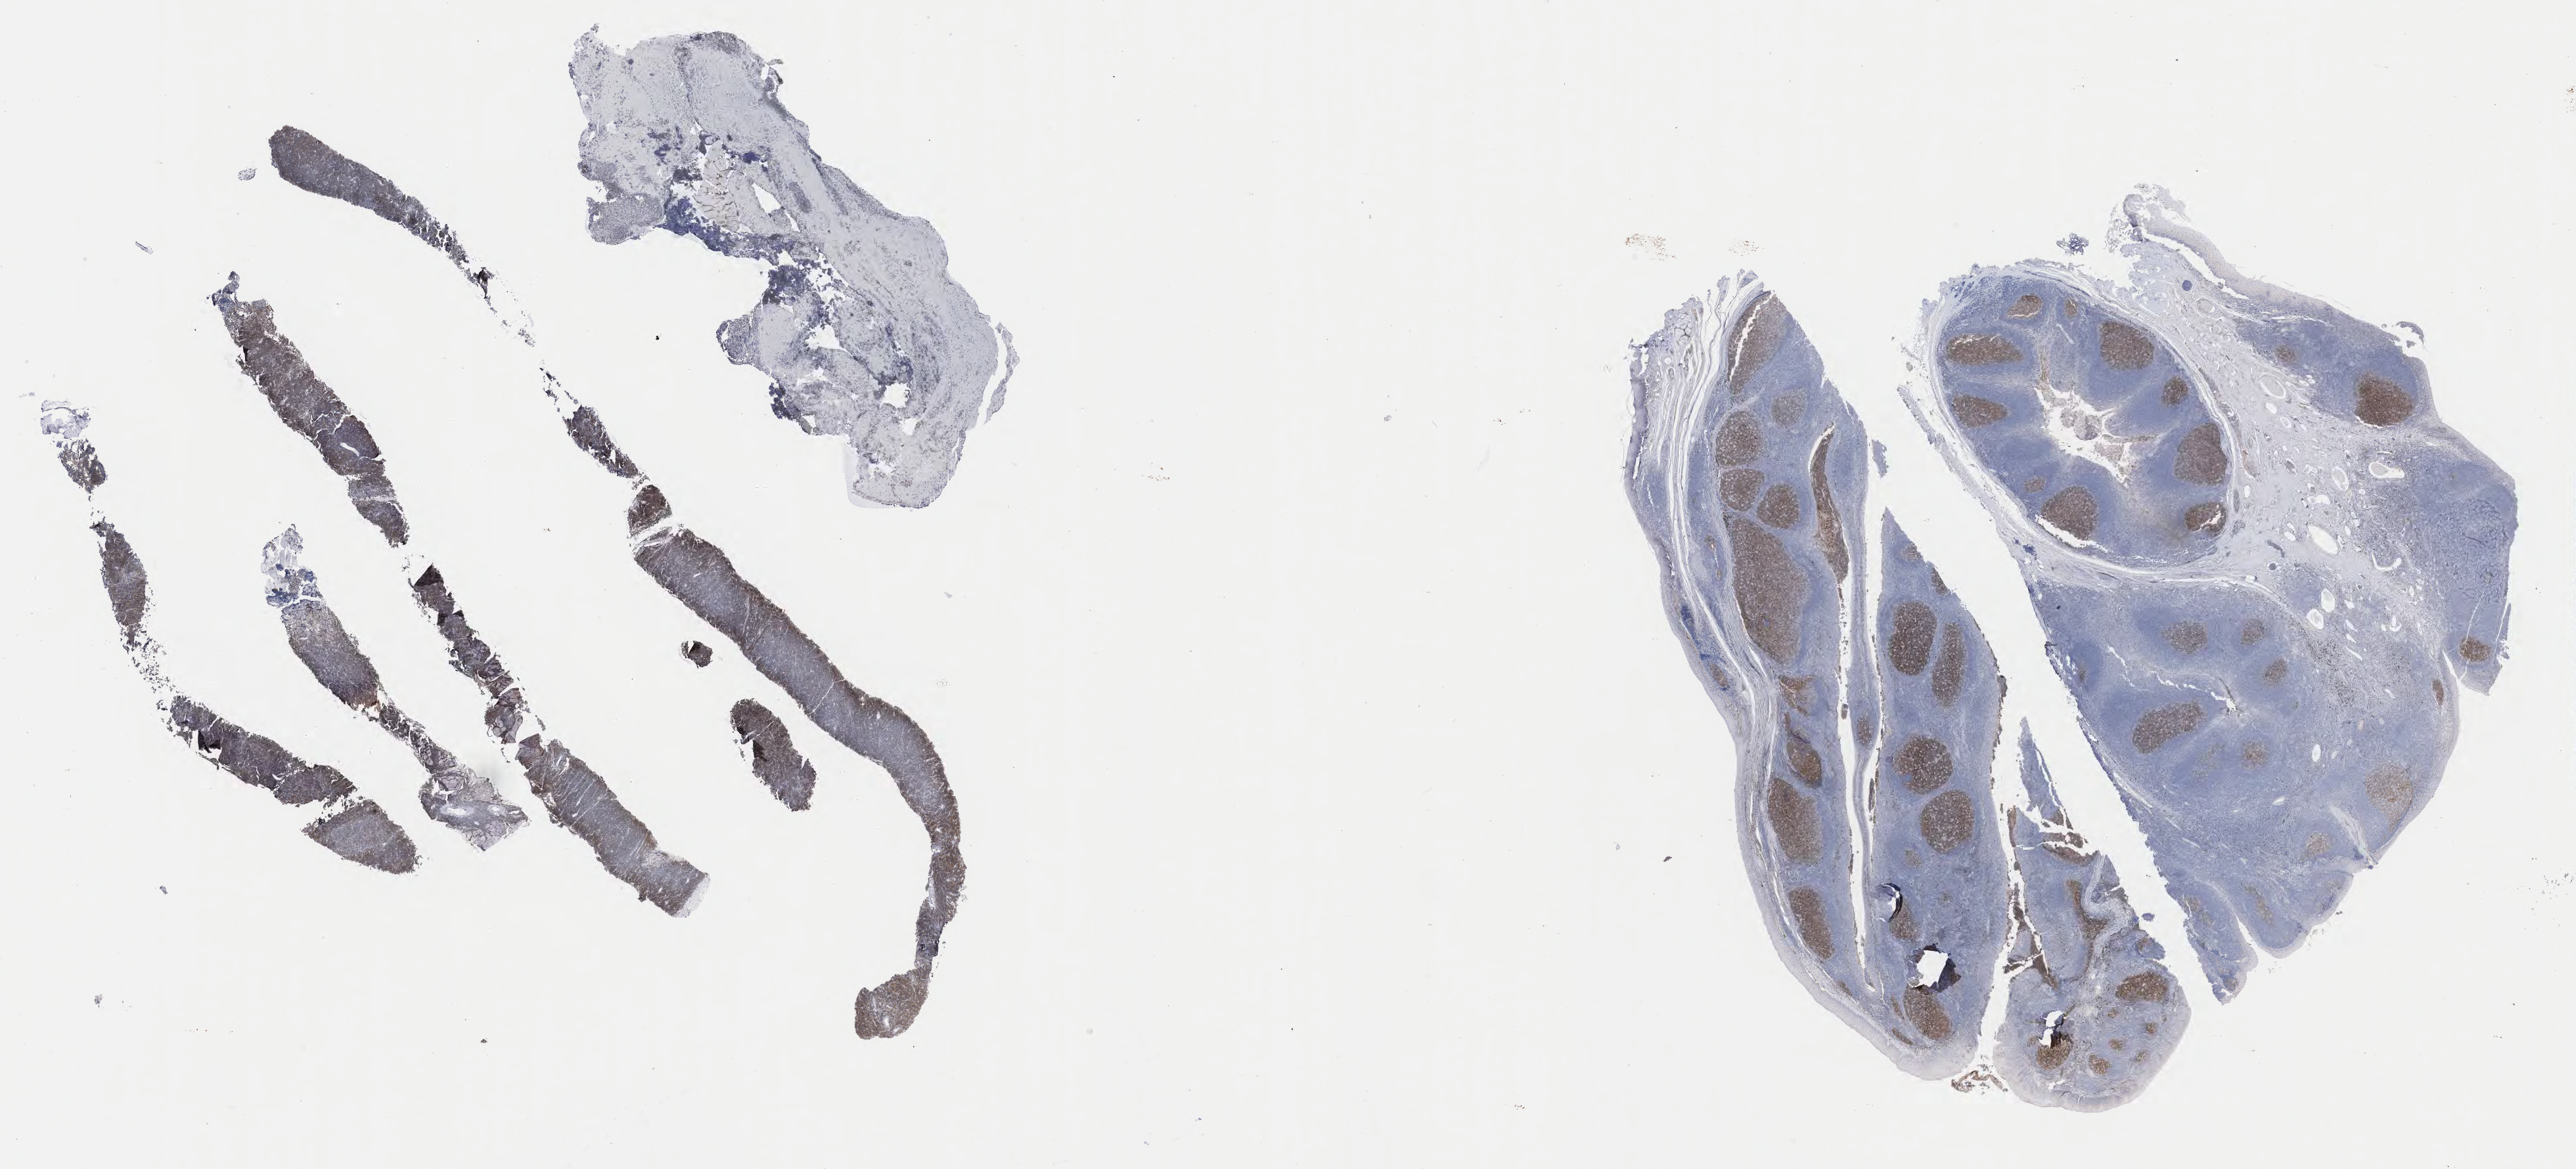
Immunohistochemistry (IHC) whole-slide image stained for CD10, low-resolution overview of the scanned area, about 31.7 x 14.4 mm. Specimen: tumor tissue. Patient male; 29 years old.
Histologic diagnosis: Burkitt lymphoma, NOS.